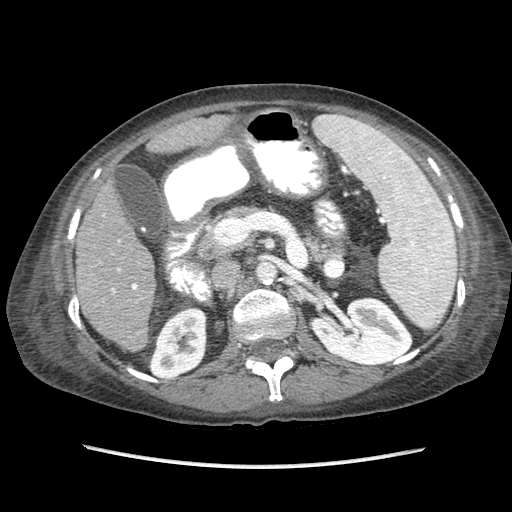
Contrast-enhanced abdominal CT (liver protocol), one axial slice. Position 35 of 87 along the scan axis. Reconstruction kernel STANDARD. Soft-tissue window (W 400 / L 40 HU). 512 × 512 image matrix, field of view 340 × 340 mm. Case-level facts recorded for this patient, not image findings: diagnosis: hepatocellular carcinoma (patient treated with transarterial chemoembolisation; whether this scan precedes or follows treatment is not stated here); TNM stage (as recorded): Stage-IIIB.
Outlined on this slice (semi-automatic segmentation, software-assisted and operator-edited):
- liver parenchyma outside the tumour (the mass and vessels are separate outlines, so this box may not span the whole liver): bounding box (x1, y1, x2, y2) in pixels: (76, 114, 234, 350)
- liver vessels: (103, 214, 138, 293)